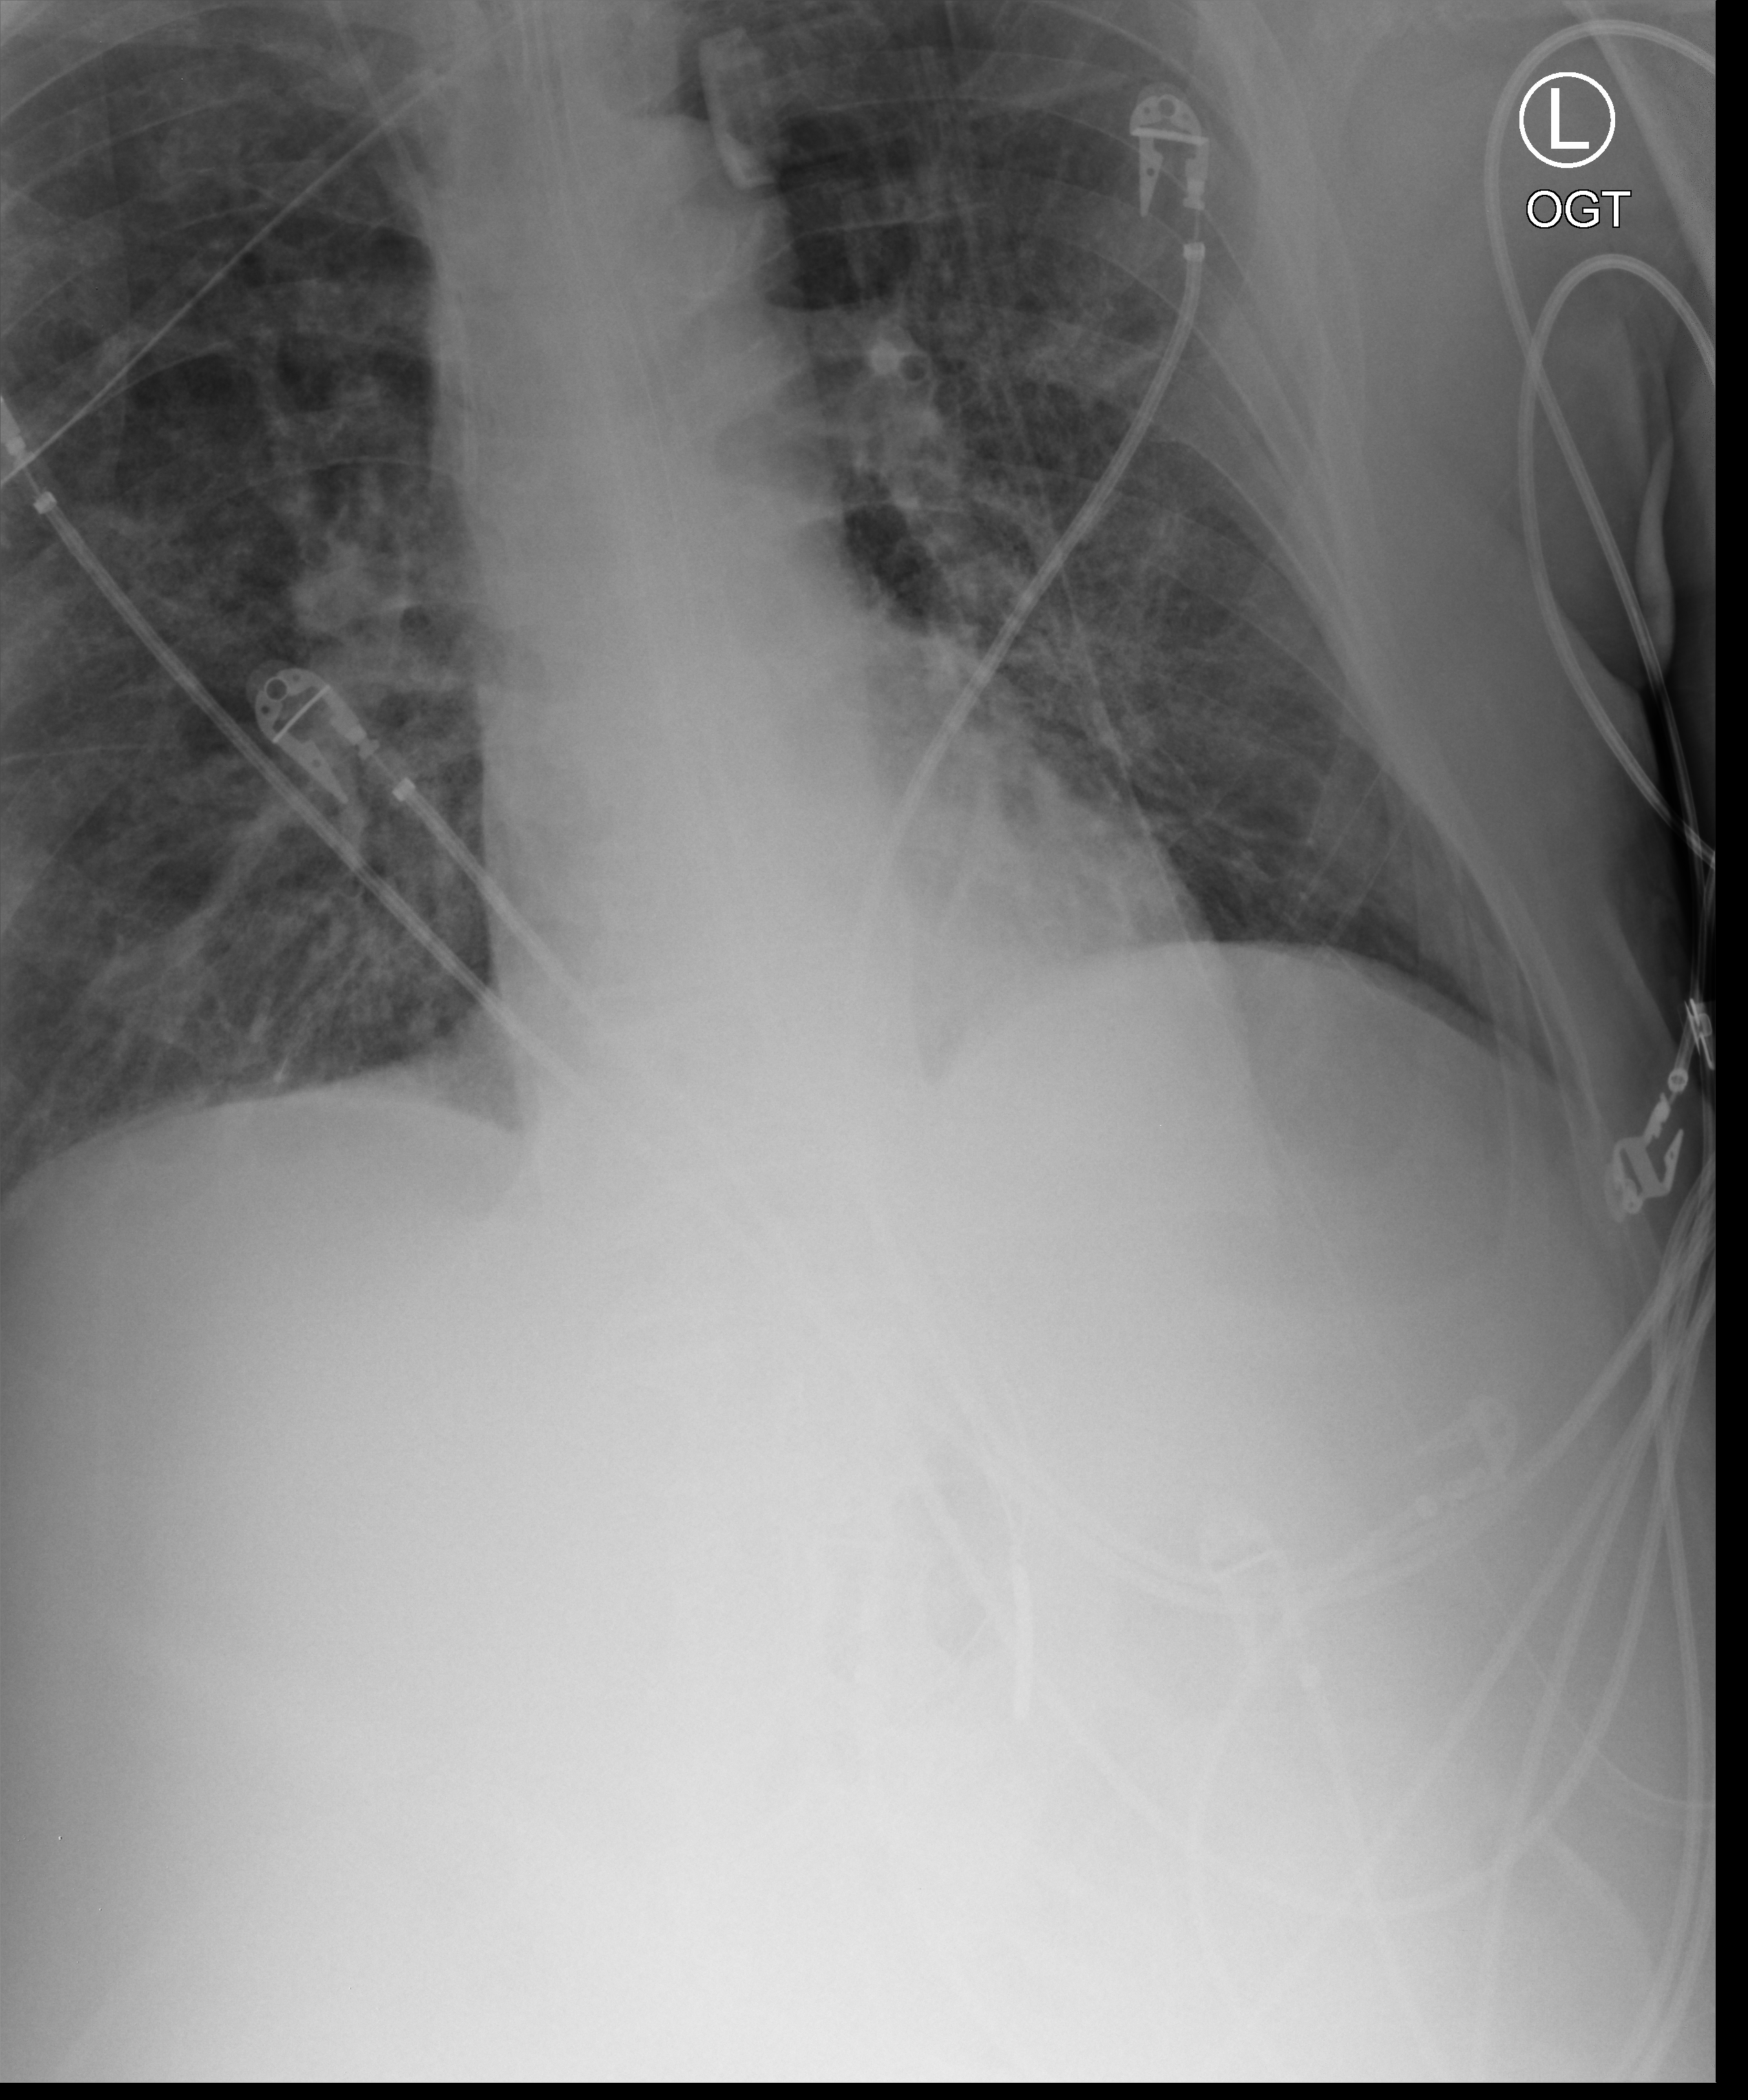
Bedside chest radiograph (computed radiography); anteroposterior (AP) projection. Patient hospitalised with COVID-19; male, aged 75–90 years.
Hospital-stay facts (about this admission, not read from this image; timing relative to this image not recorded): length of hospital stay: 26 days.